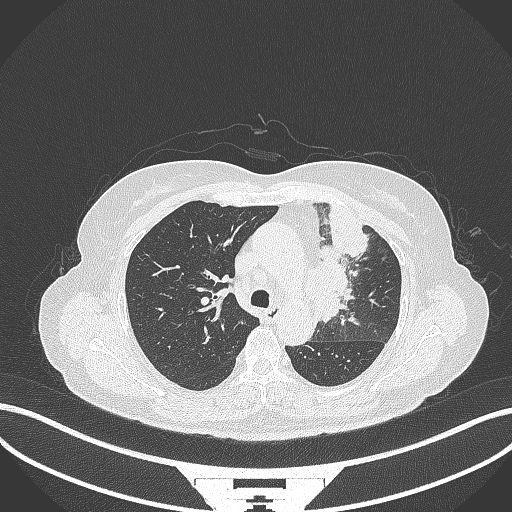
Chest CT, one axial slice. Position 230 of 382 along the scan axis. Reconstruction kernel B70f. 120 kVp. Lung window (W 1500 / L -600 HU). 1 mm slice thickness. 512 × 512 image matrix. Patient: female, 64 years. Case-level facts recorded for this patient, not image findings: clinical TNM (as recorded): T2a N2 M0.
Annotated regions visible in this slice (rectangle marked by the reading radiologist):
- lung tumour (recorded histology: adenocarcinoma): bounding box (x1, y1, x2, y2) in pixels: (308, 218, 371, 324)